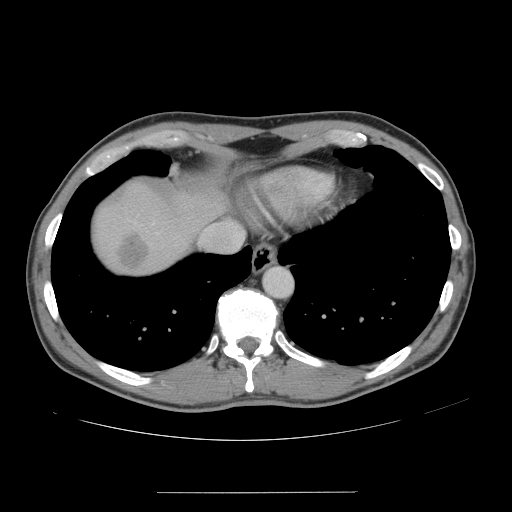
Contrast-enhanced abdominal CT, one axial slice; slice 138 of 178 in the series (ordered by position); 120 kVp; intravenous contrast given; soft-tissue window (W 400 / L 40 HU); 512 × 512 image matrix, field of view 401 × 401 mm. Male patient, age 53 years. From the clinical record (not read from this slice): diagnosis: colorectal cancer liver metastases, imaged before liver resection; multiple liver metastases: yes; largest metastasis: 2.4 cm; chemotherapy before resection: yes.
Structures marked on this image (expert manual segmentation):
- liver: bounding box [x1, y1, x2, y2] px = [93, 183, 228, 274]
- planned liver remnant (the part of the liver to remain after resection): [195, 192, 229, 214]
- liver metastasis: [118, 235, 147, 268]